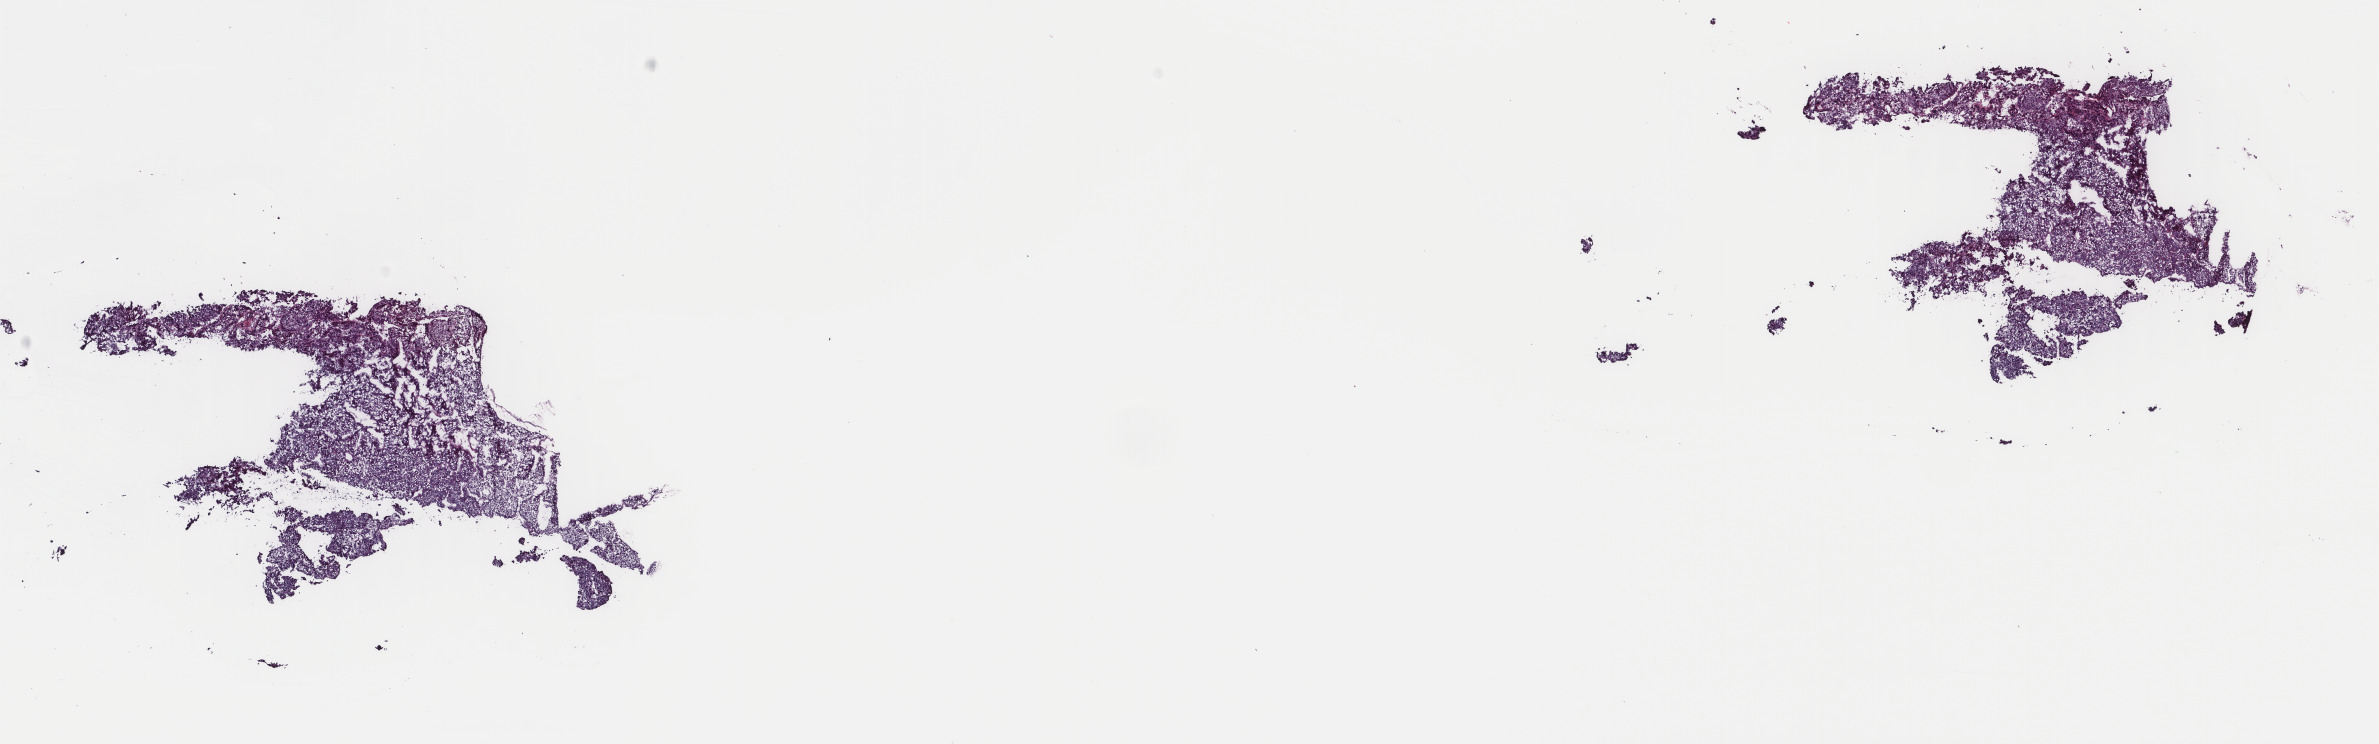
Whole-slide histology image, H&E, shown as a low-resolution overview of the whole scanned area (about 18.9 x 5.9 mm, from a 40x scan). Frozen section. Liver, primary tumour sample. Male, age 48 years at initial diagnosis. Histologic grade: G2 (moderately differentiated). Pathologist review of this section (percent, as recorded): tumour cells 93%, tumour nuclei 95%, normal cells 0%, stromal cells 5%, necrosis 2%. Infiltration values recorded for this section: lymphocyte infiltration 1%, monocyte infiltration 0%, neutrophil infiltration 0%.
AJCC pathologic stage: IIIB. Pathologic diagnosis: Hepatocellular carcinoma, NOS.